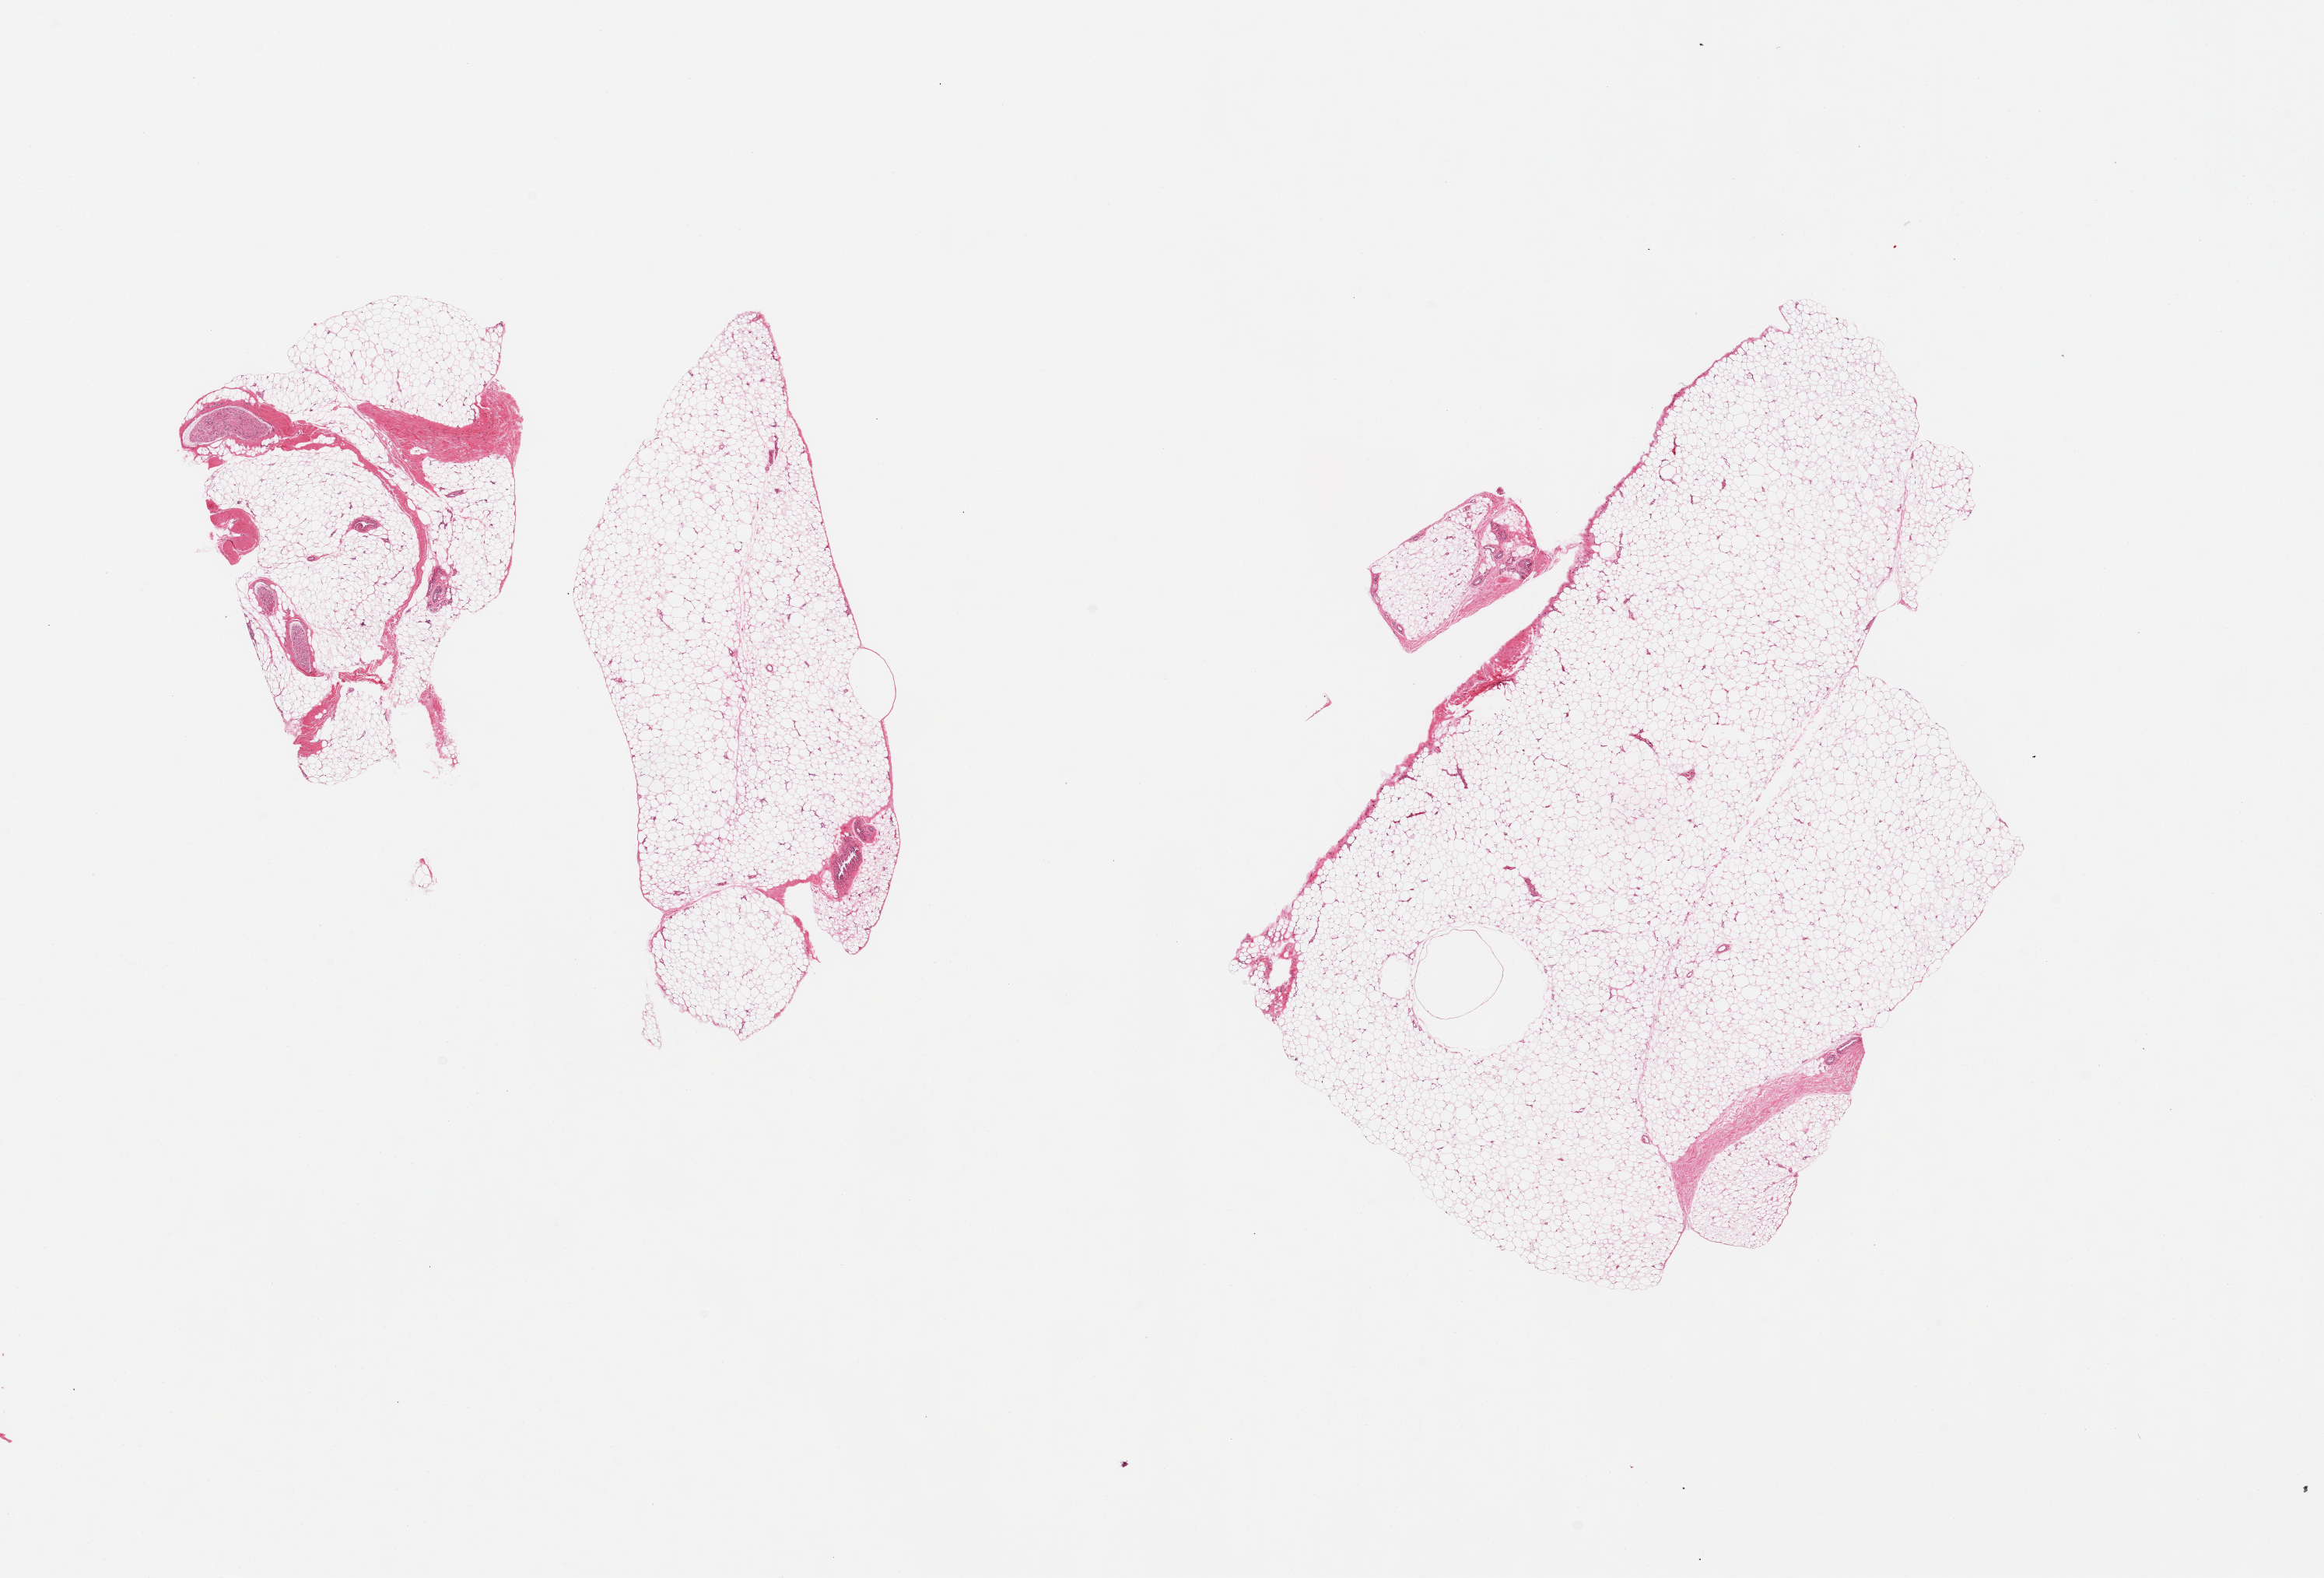
Whole-slide image, H&E stain, brightfield, low-resolution overview of the scanned area, about 23.6 x 16.0 mm (acquisition: 20x scan). PAXgene-fixed paraffin-embedded (PFPE) section. Section of adipose tissue (target tissue). Tissue donor sample.
Pathologist's review note for this sample: 3 pieces; mature adipose tissue with trace of fibrovascular component and nerves.